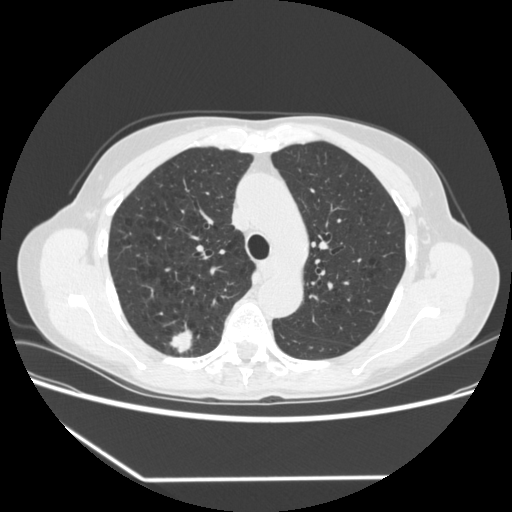
Low-dose screening chest CT, axial slice. First (baseline) screen. Lung window (W 1500 / L -600 HU). Slice 239 of 323 in the series. 512 × 512 image matrix, field of view 360 × 360 mm. Female, age 67 years at enrolment. Current smoker at enrolment.
- Expert reader's lesion annotation, bounding box <157,324,201,361> (left, top, right, bottom; pixels).
- The screening reader recorded 2 non-calcified nodules or masses ≥4 mm on this exam (right upper lobe, right lower lobe); which of them this box marks is not recorded.
- Official screen result: positive, change unspecified: nodule(s) >= 4 mm or enlarging nodule(s), mass(es), or other non-specific abnormalities suspicious for lung cancer.